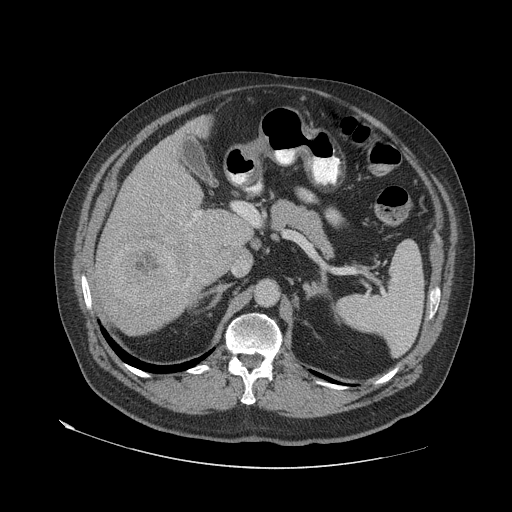
Contrast-enhanced abdominal CT (liver protocol), one axial slice. Soft-tissue window (W 400 / L 40 HU). 2.5 mm slice thickness. 512 × 512 image matrix. Case-level facts recorded for this patient, not image findings: diagnosis: hepatocellular carcinoma (patient treated with transarterial chemoembolisation; whether this scan precedes or follows treatment is not stated here); TNM stage (as recorded): Stage-IVA; Child-Pugh class: A; tumour nodularity: multinodular.
Outlined on this slice (semi-automatic segmentation, software-assisted and operator-edited):
- liver parenchyma outside the tumour (the mass and vessels are separate outlines, so this box may not span the whole liver): bounding box (x1, y1, x2, y2) in pixels: (92, 116, 255, 334)
- mass: (106, 234, 183, 305)
- liver vessels: (193, 212, 201, 221)